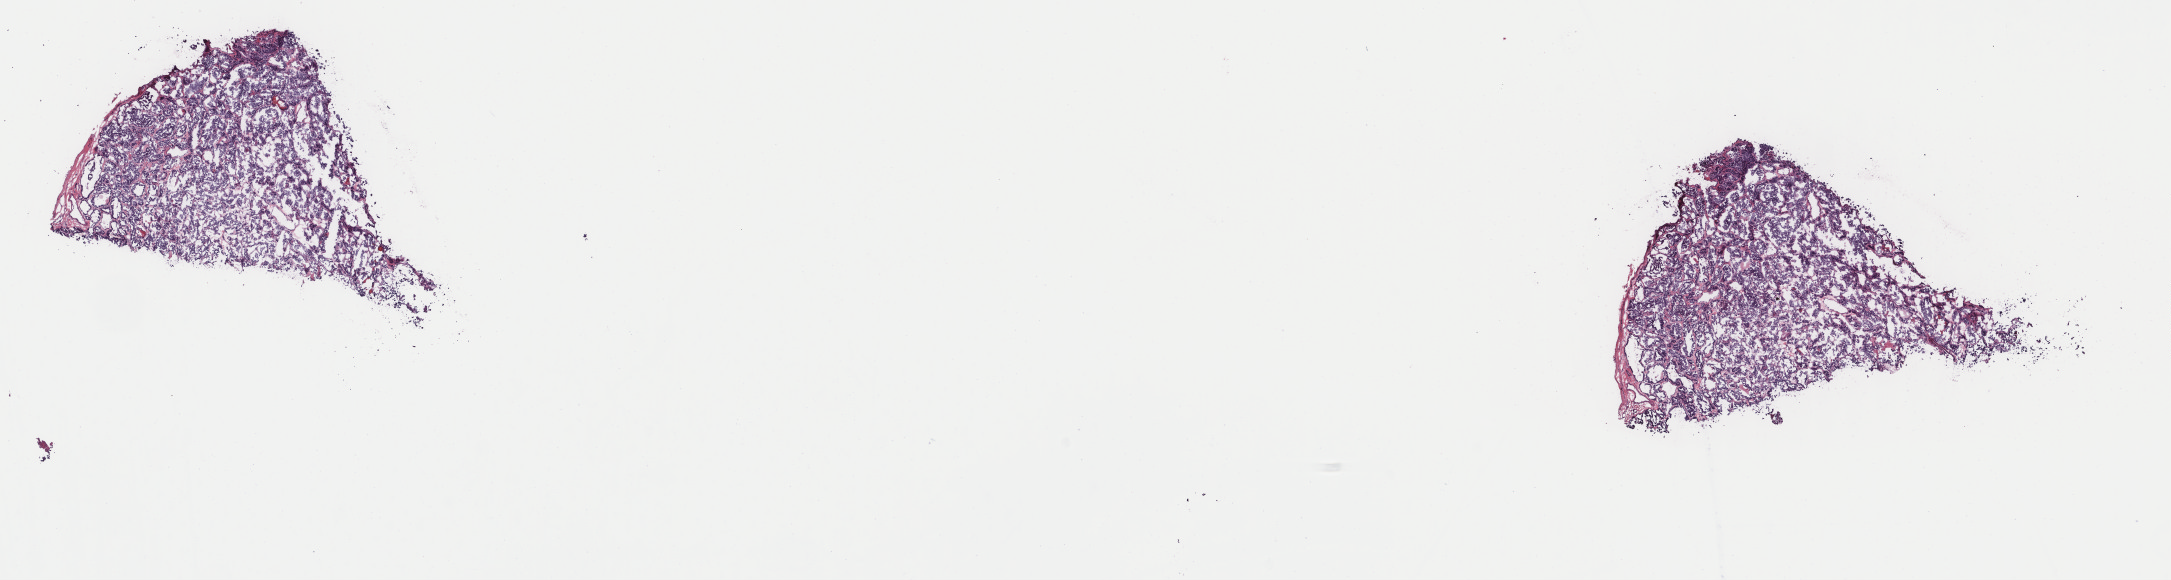
Whole-slide histology image, H&E-stained, a low-resolution overview of the entire scanned area, about 17.2 x 4.6 mm (acquisition: 40x scan); frozen section from the top of the tissue portion; thyroid, primary tumour sample. Patient: female, age at initial diagnosis 36 years. Composition of this section per pathologist review: tumour cells 100%, tumour nuclei 95%, normal cells 0%, stromal cells 0%, necrosis 0%. Inflammatory infiltration, as recorded: lymphocyte infiltration 0%, monocyte infiltration 0%, neutrophil infiltration 0%.
Pathologic diagnosis: Papillary adenocarcinoma, NOS (thyroid gland). AJCC pathologic stage: I (7th edition).